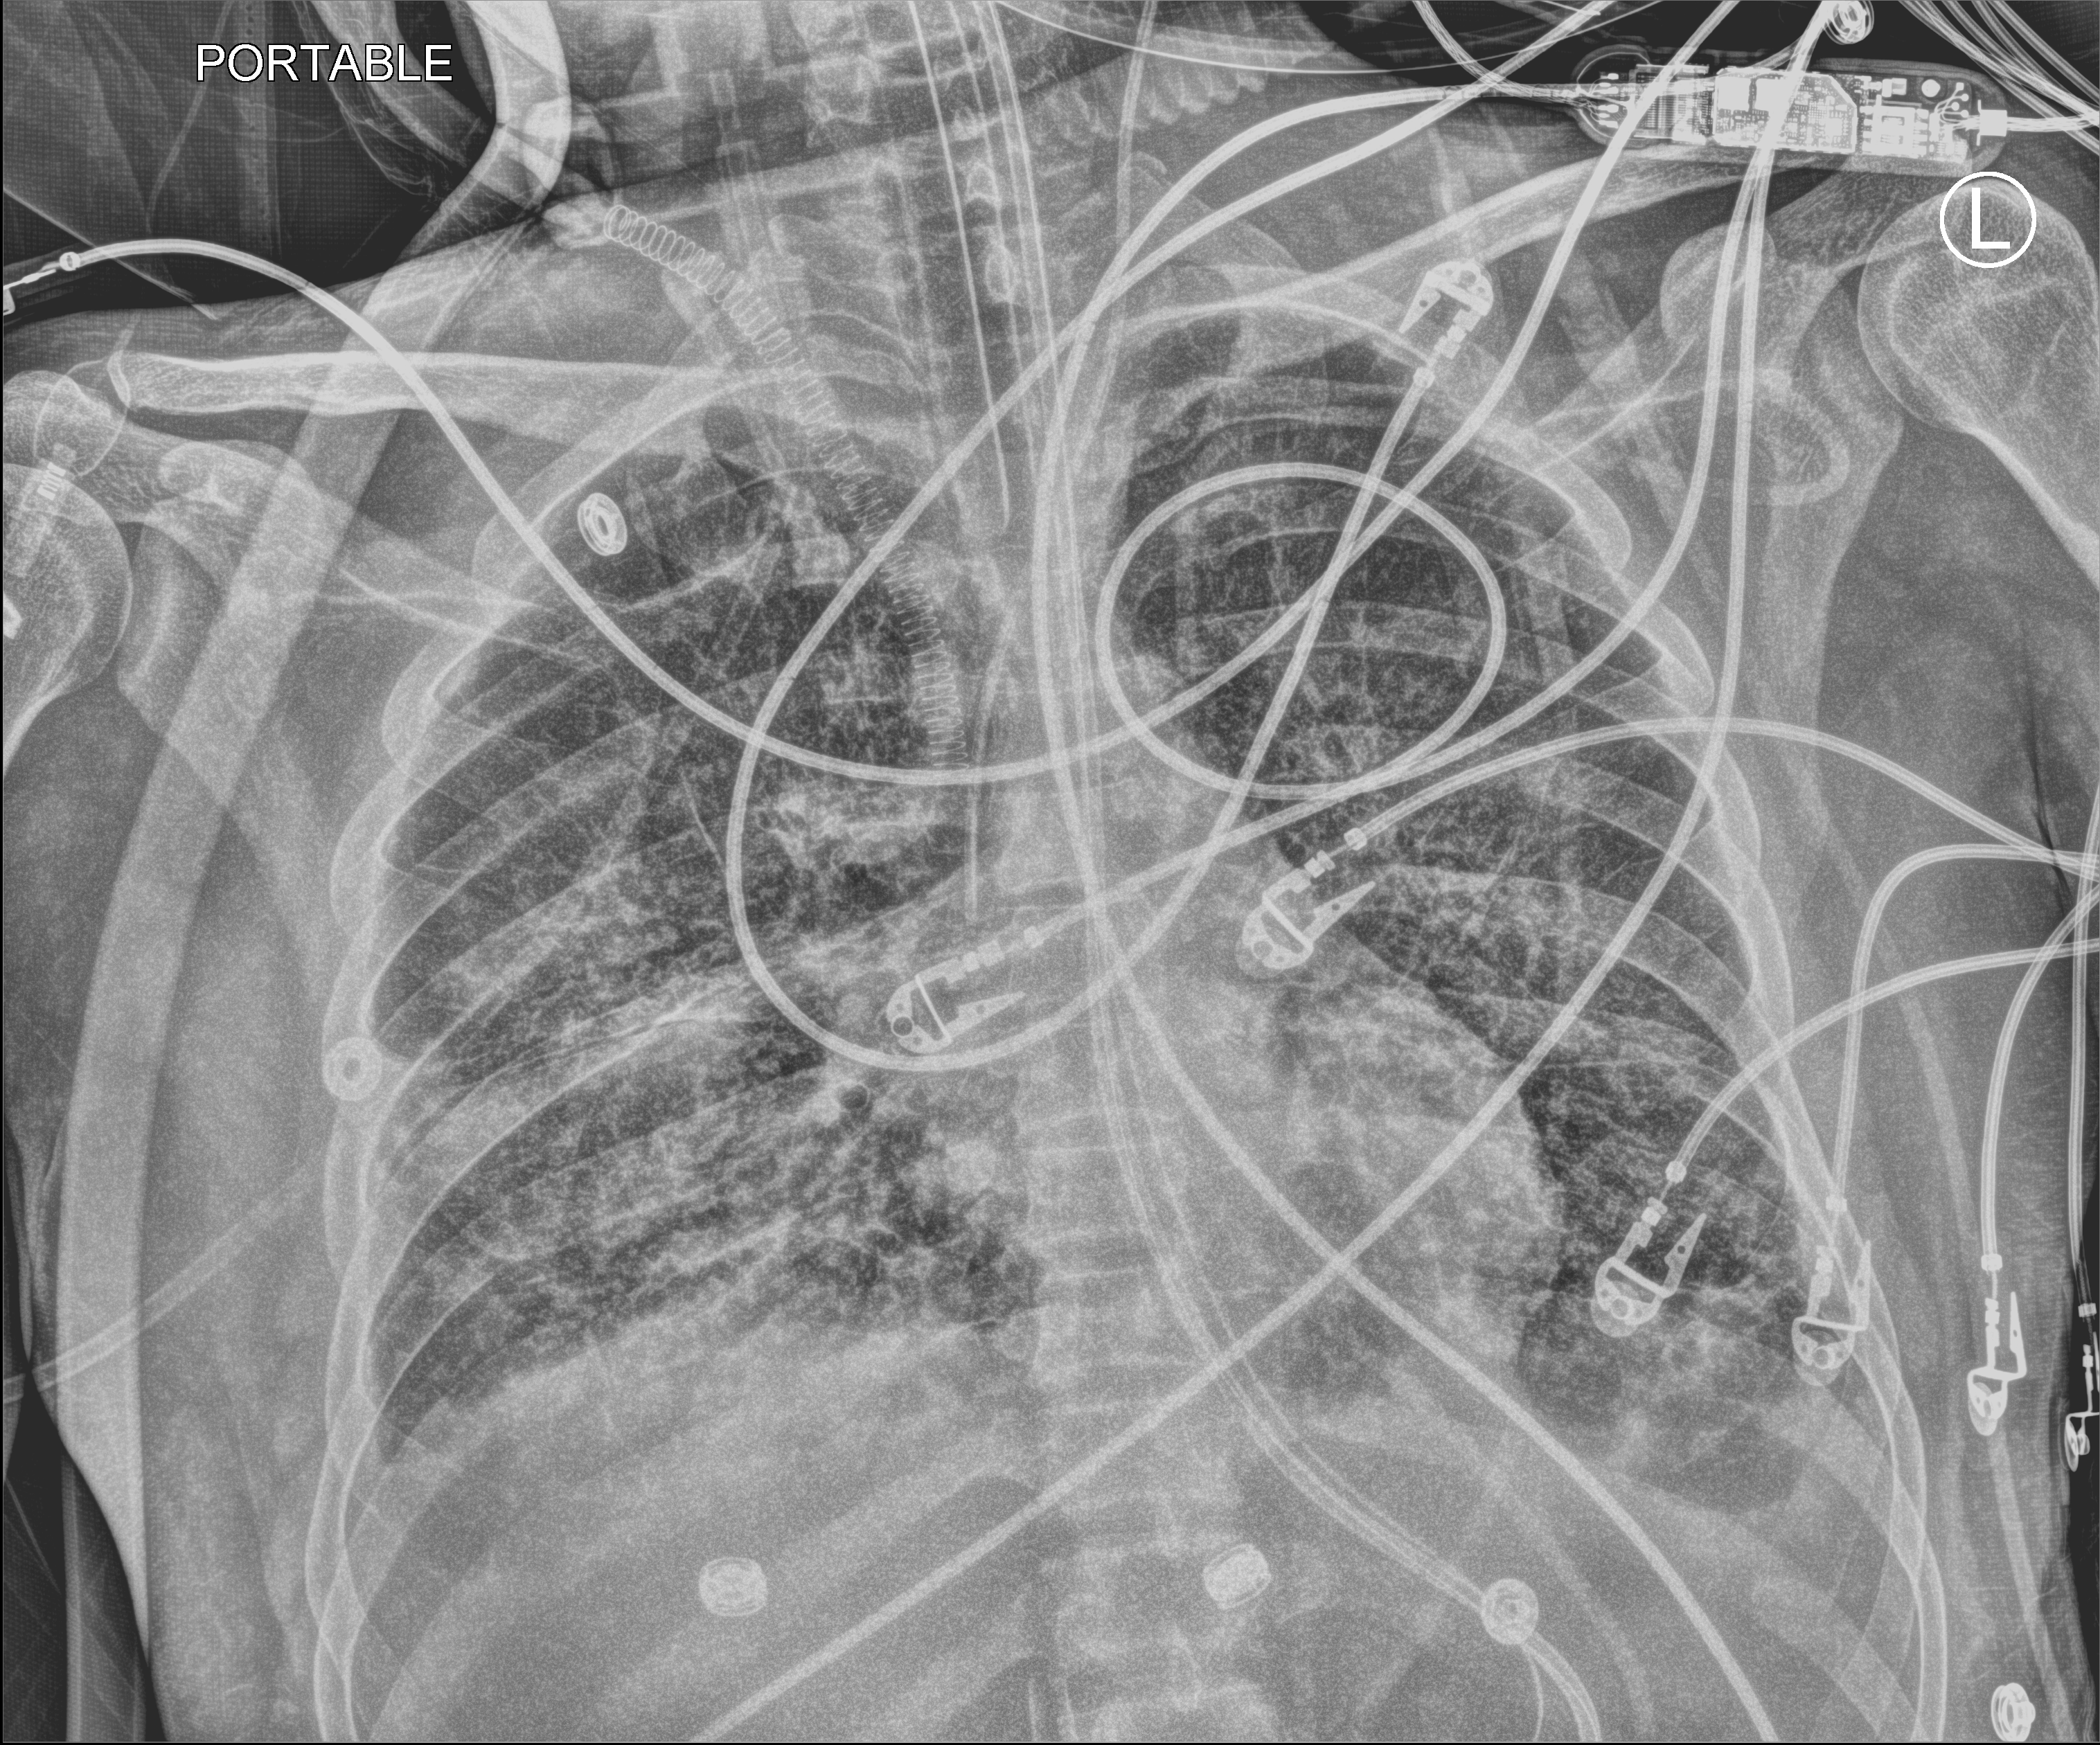
Chest X-ray (portable); anteroposterior (AP) projection. Adult patient hospitalised with COVID-19, age 18–59 years.
Hospital-stay facts (about this admission, not read from this image; timing relative to this image not recorded): mechanically ventilated during this hospital stay: yes; length of hospital stay: 60 days; admitted to intensive care during this hospital stay: yes.